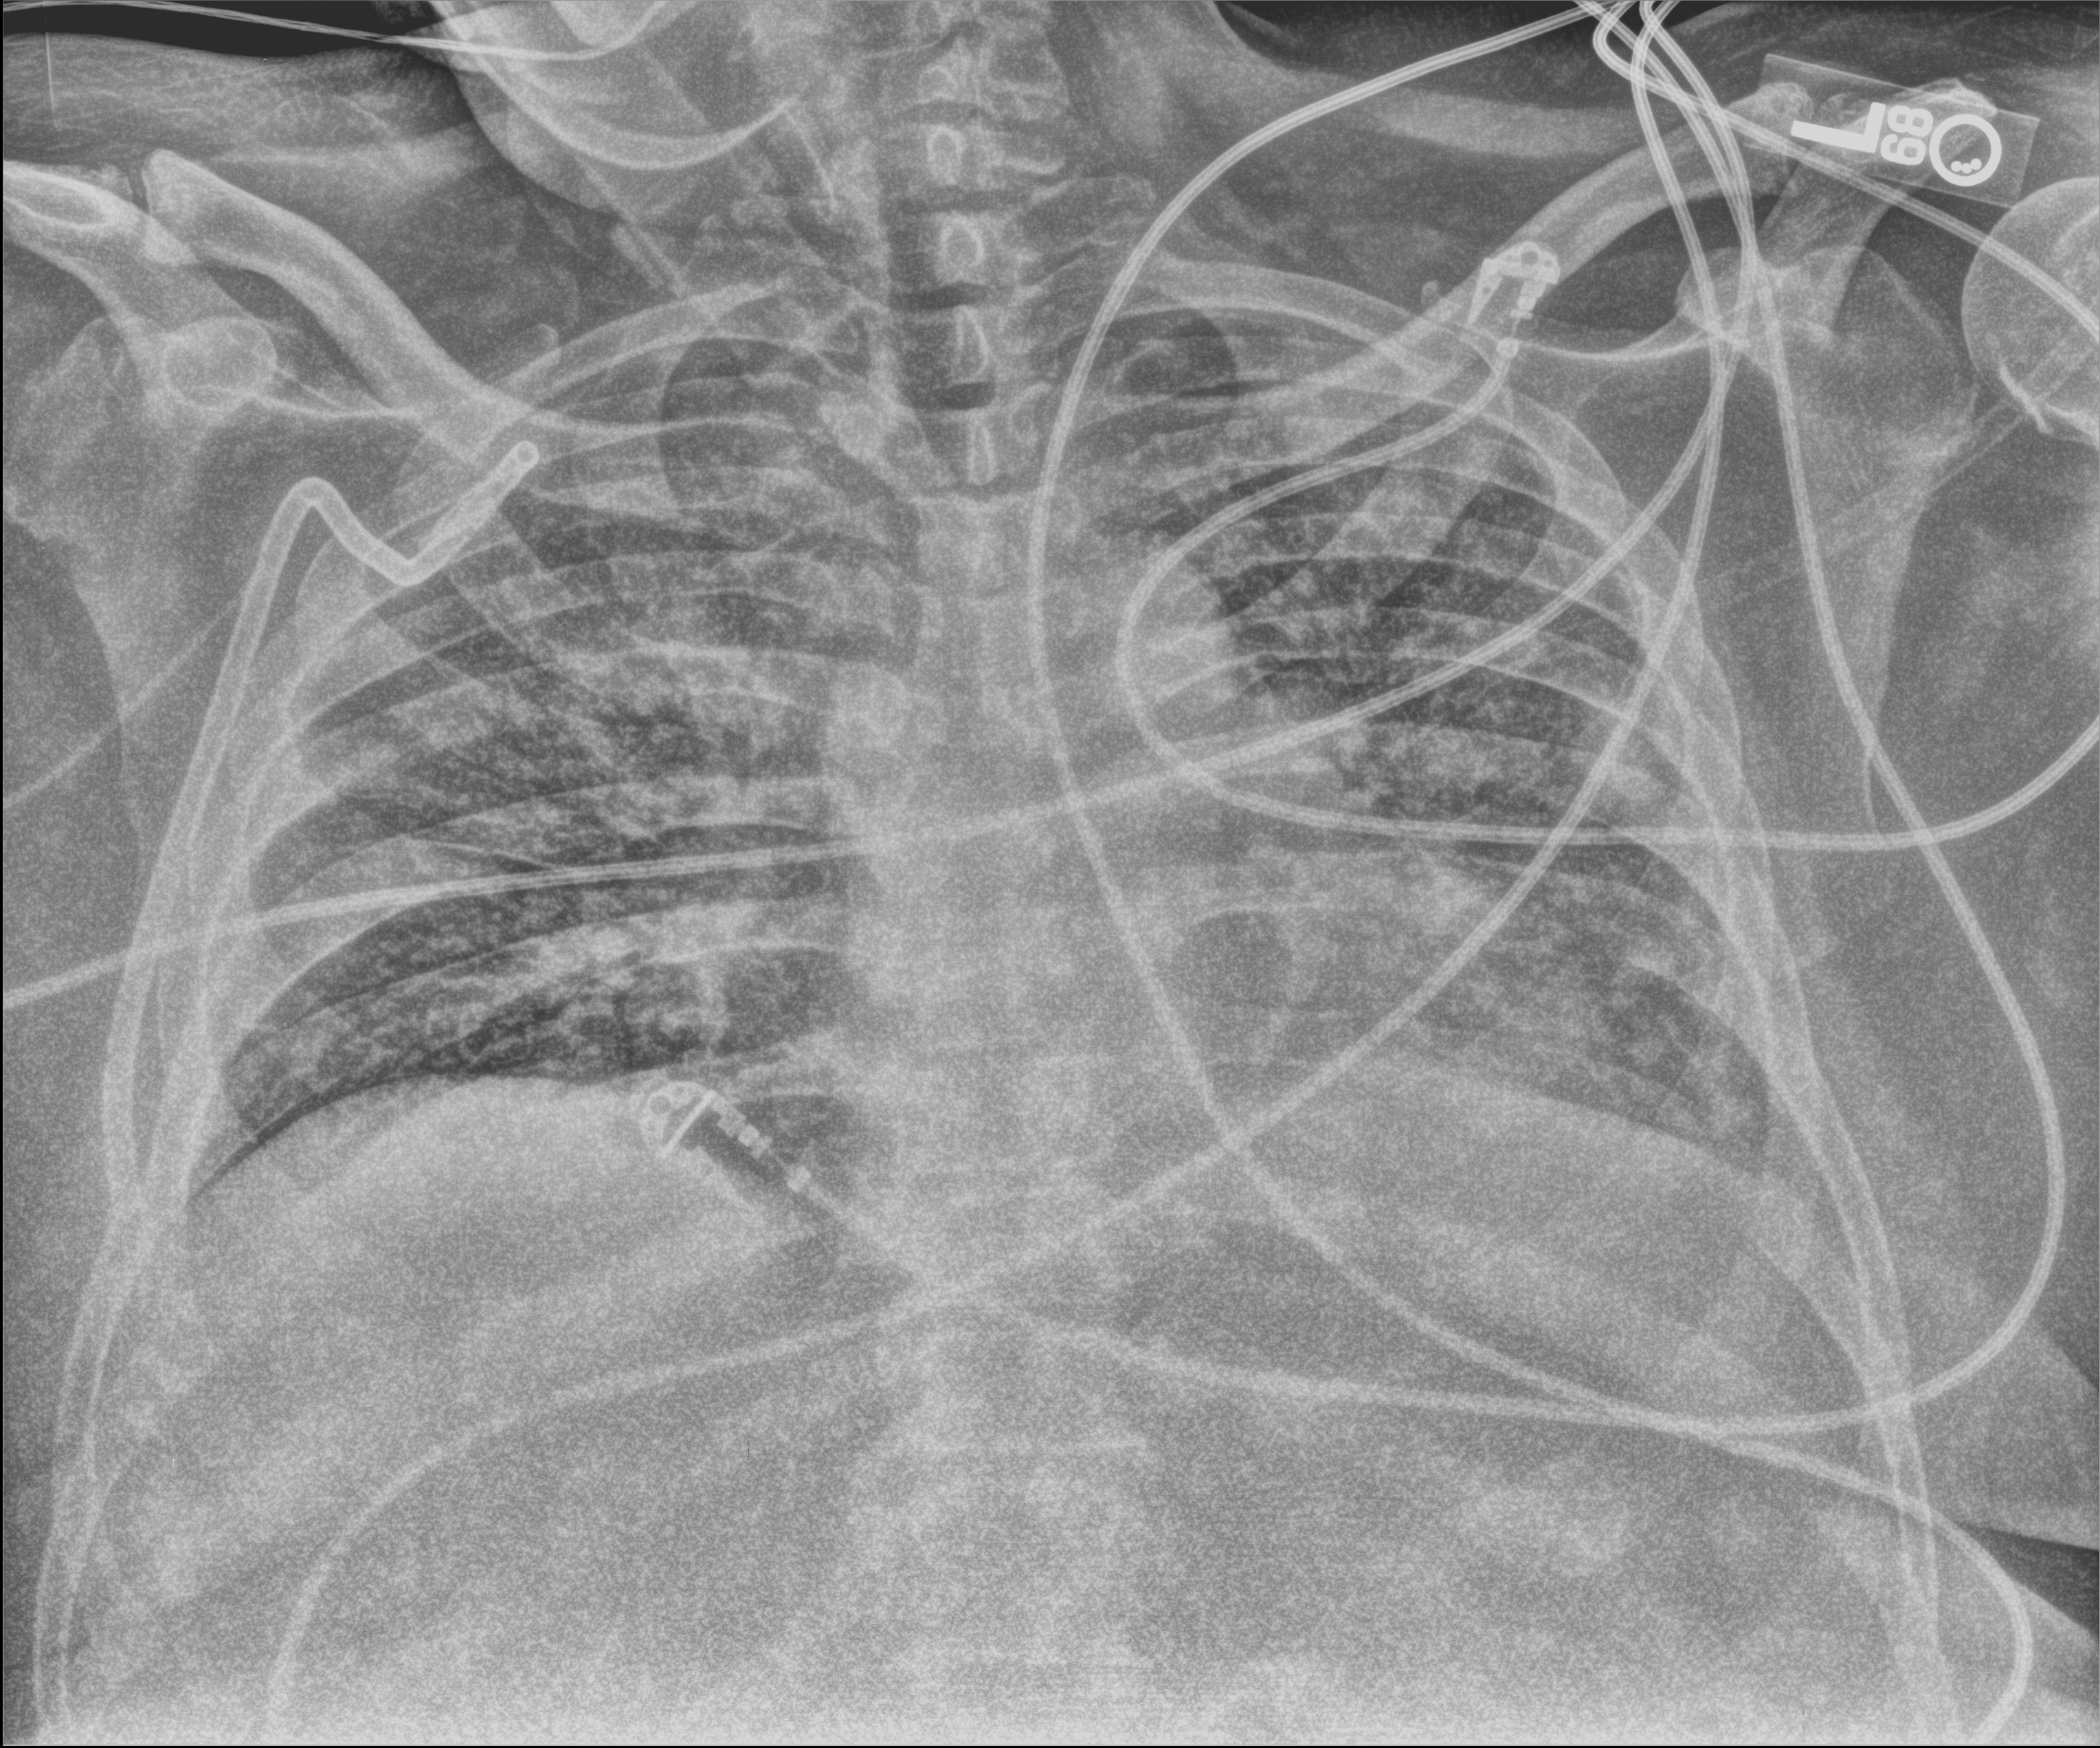
Bedside chest radiograph (computed radiography), anteroposterior (AP) projection. Patient hospitalised with COVID-19; male, aged 60–74 years.
Hospital-stay facts (about this admission, not read from this image; timing relative to this image not recorded): mechanically ventilated during this hospital stay: yes; length of hospital stay: 34 days.